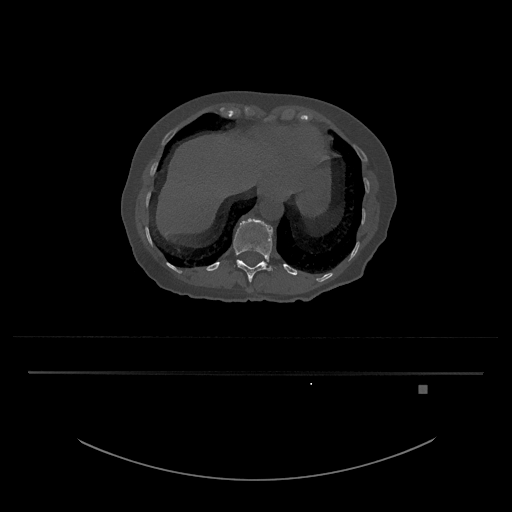
CT including the spine, one axial slice; position 610 of 797 along the scan axis; reconstruction kernel Br40s/3; bone window (W 1800 / L 400 HU); 512 × 512 image matrix, field of view 500 × 500 mm. Patient: female, 57 years. Case-level facts recorded for this patient, not image findings: primary cancer: cervical.
Outlined on this slice (semi-automatically segmented with operator editing):
- T12 vertebra: box from (x=233, y=218) to (x=273, y=282) px